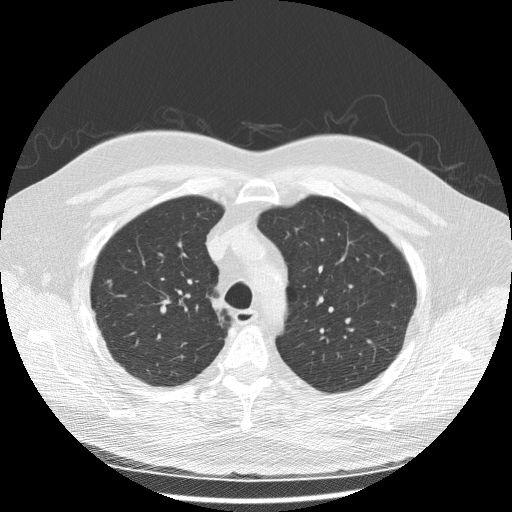
Low-dose screening chest CT, one axial slice. Position 188 of 243 along the scan axis. Reconstruction kernel STANDARD. Lung window (W 1500 / L -600 HU). 2.5 mm slice thickness. 512 × 512 image matrix, field of view 380 × 380 mm.
Outlined on this slice (manually delineated by an expert):
- lesion 1 (tumor, upper lobe of right lung): box from (x=107, y=279) to (x=112, y=287) px